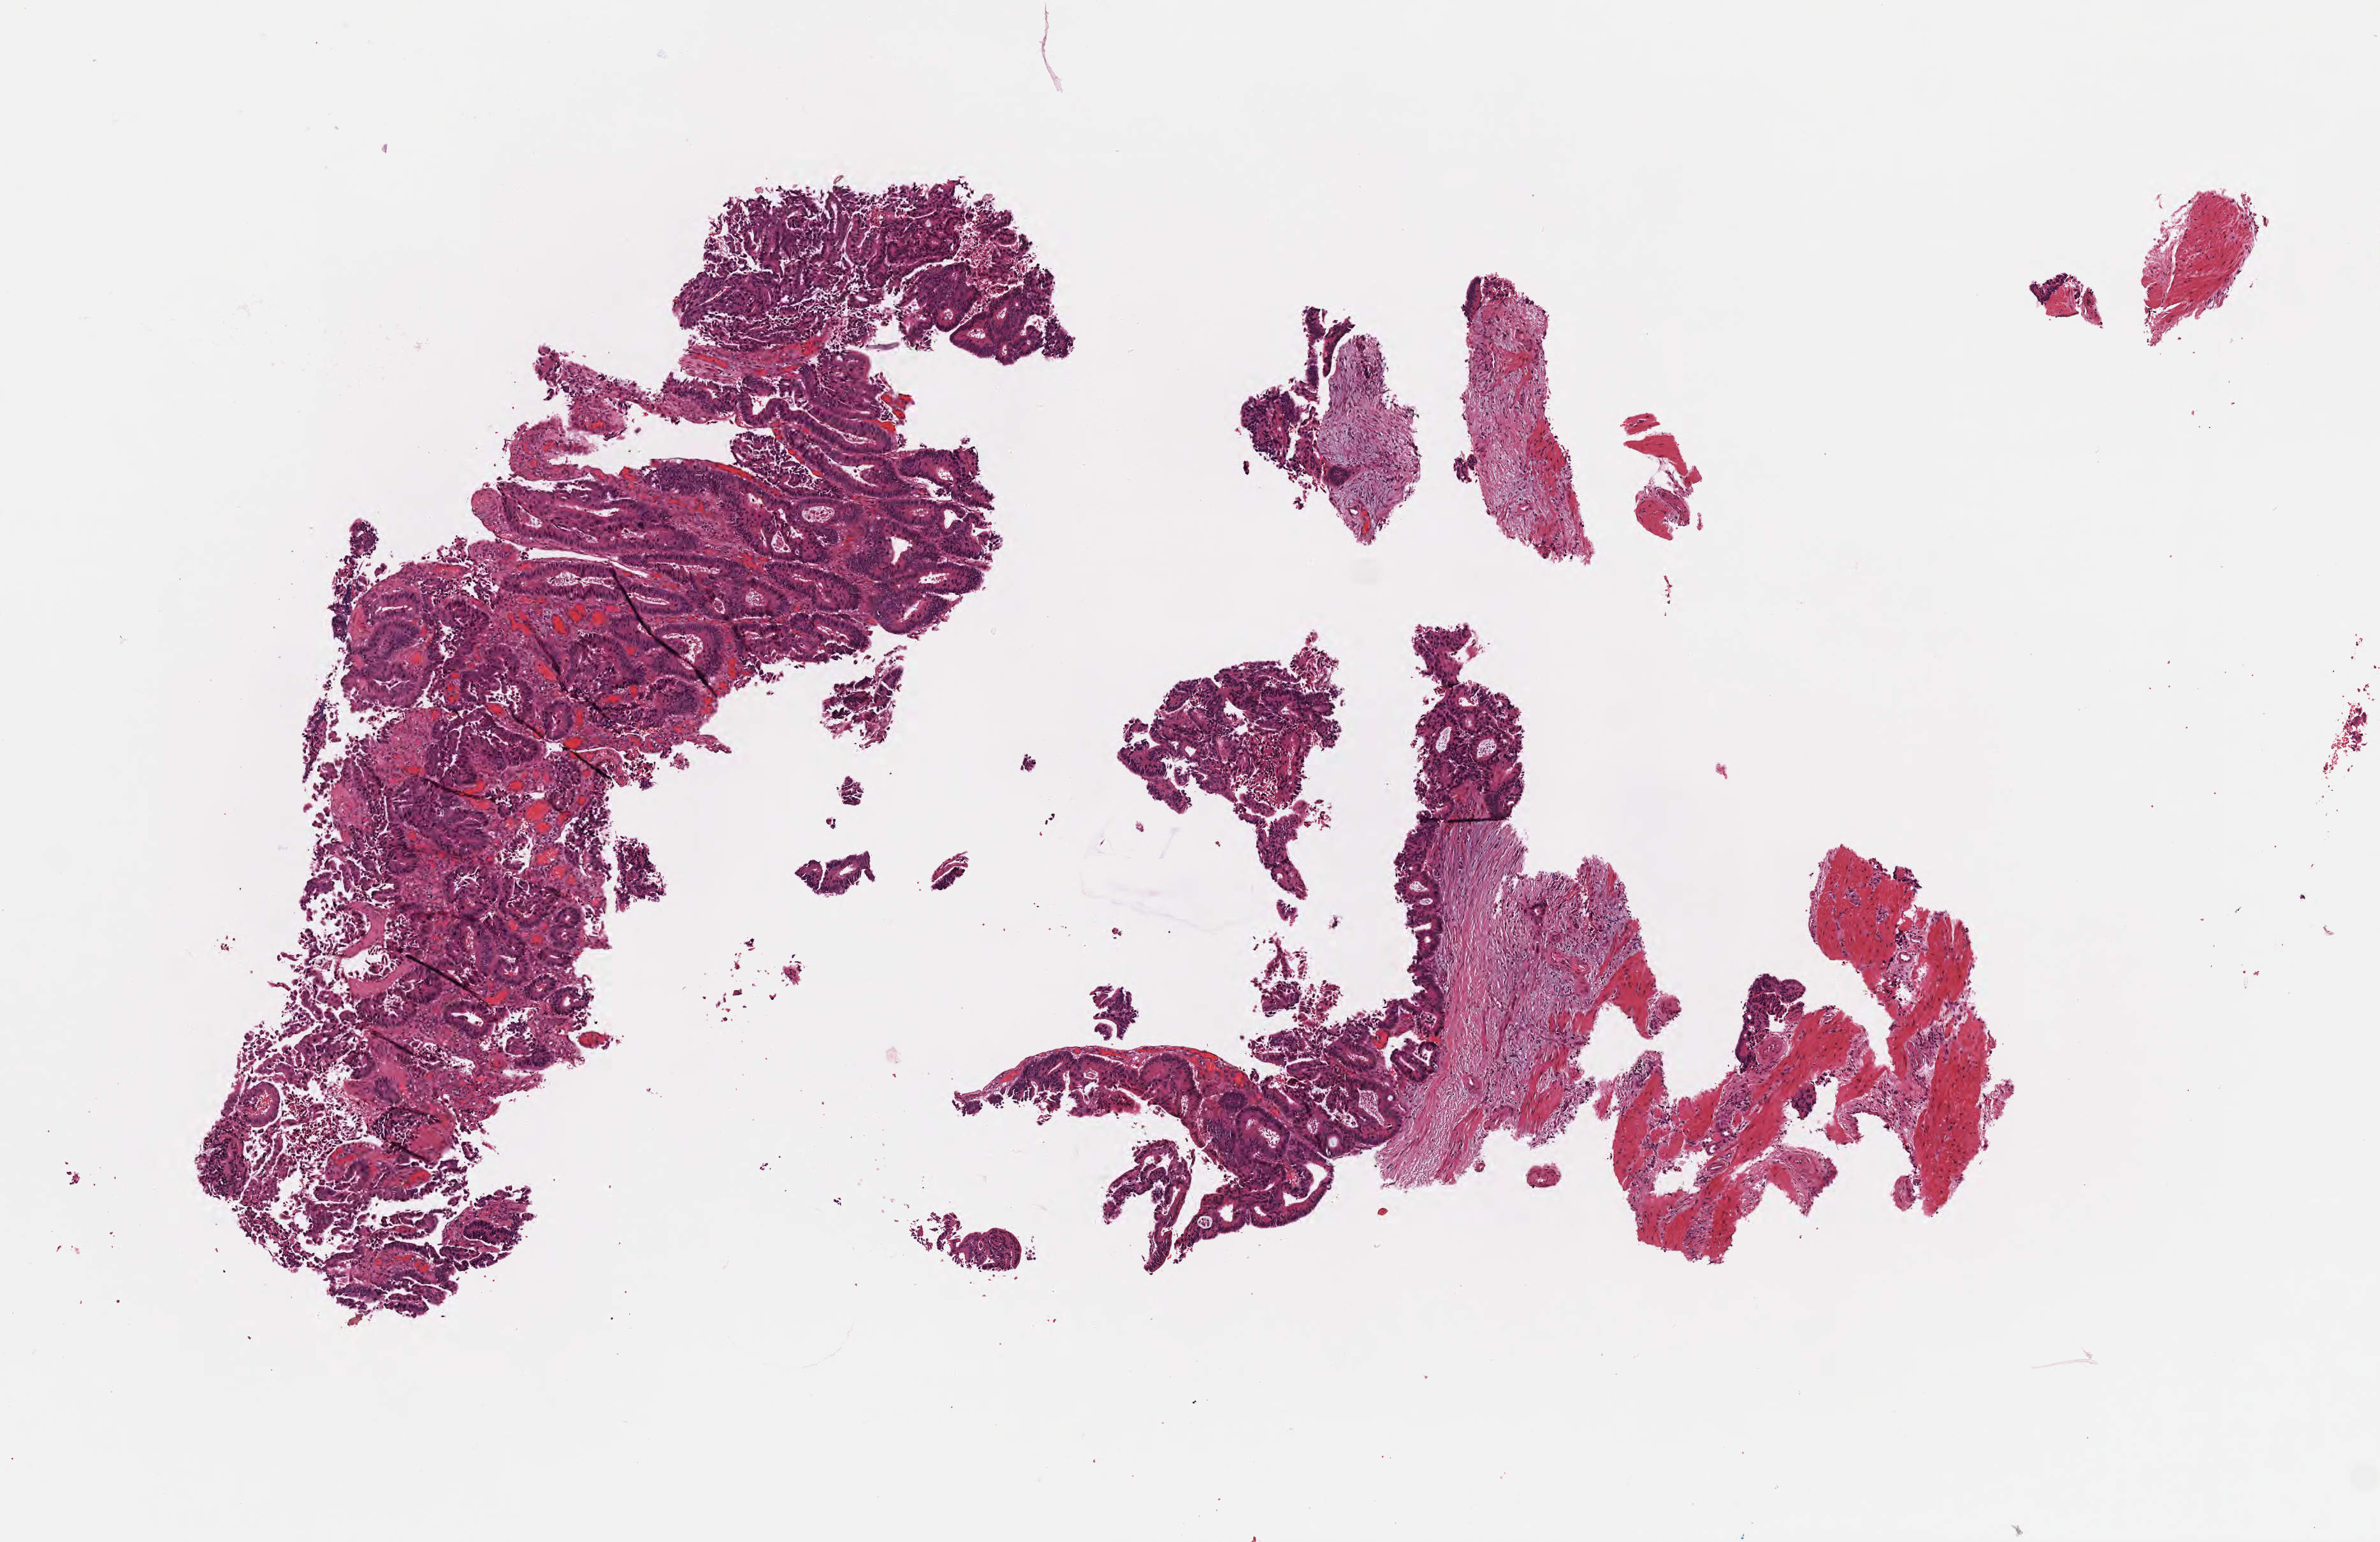
Digitized H&E-stained section, shown as a low-resolution overview of the whole scanned area (about 7.6 x 4.9 mm). FFPE section. Primary tumor. Anatomic site: cecum. Patient: male, age at initial diagnosis 71 years. Tumor grade: G2 (moderately differentiated). Composition of this section per pathologist review: tumor cells 80%, tumor nuclei 80%, stromal cells 18%, necrosis 2%, normal cells 0%. Inflammatory infiltration, as recorded: lymphocyte infiltration 5%, monocyte infiltration 1%, neutrophil infiltration 7%.
Section: top of the tissue portion. Histologic diagnosis: Adenocarcinoma, NOS. AJCC pathologic stage: Stage IIA.